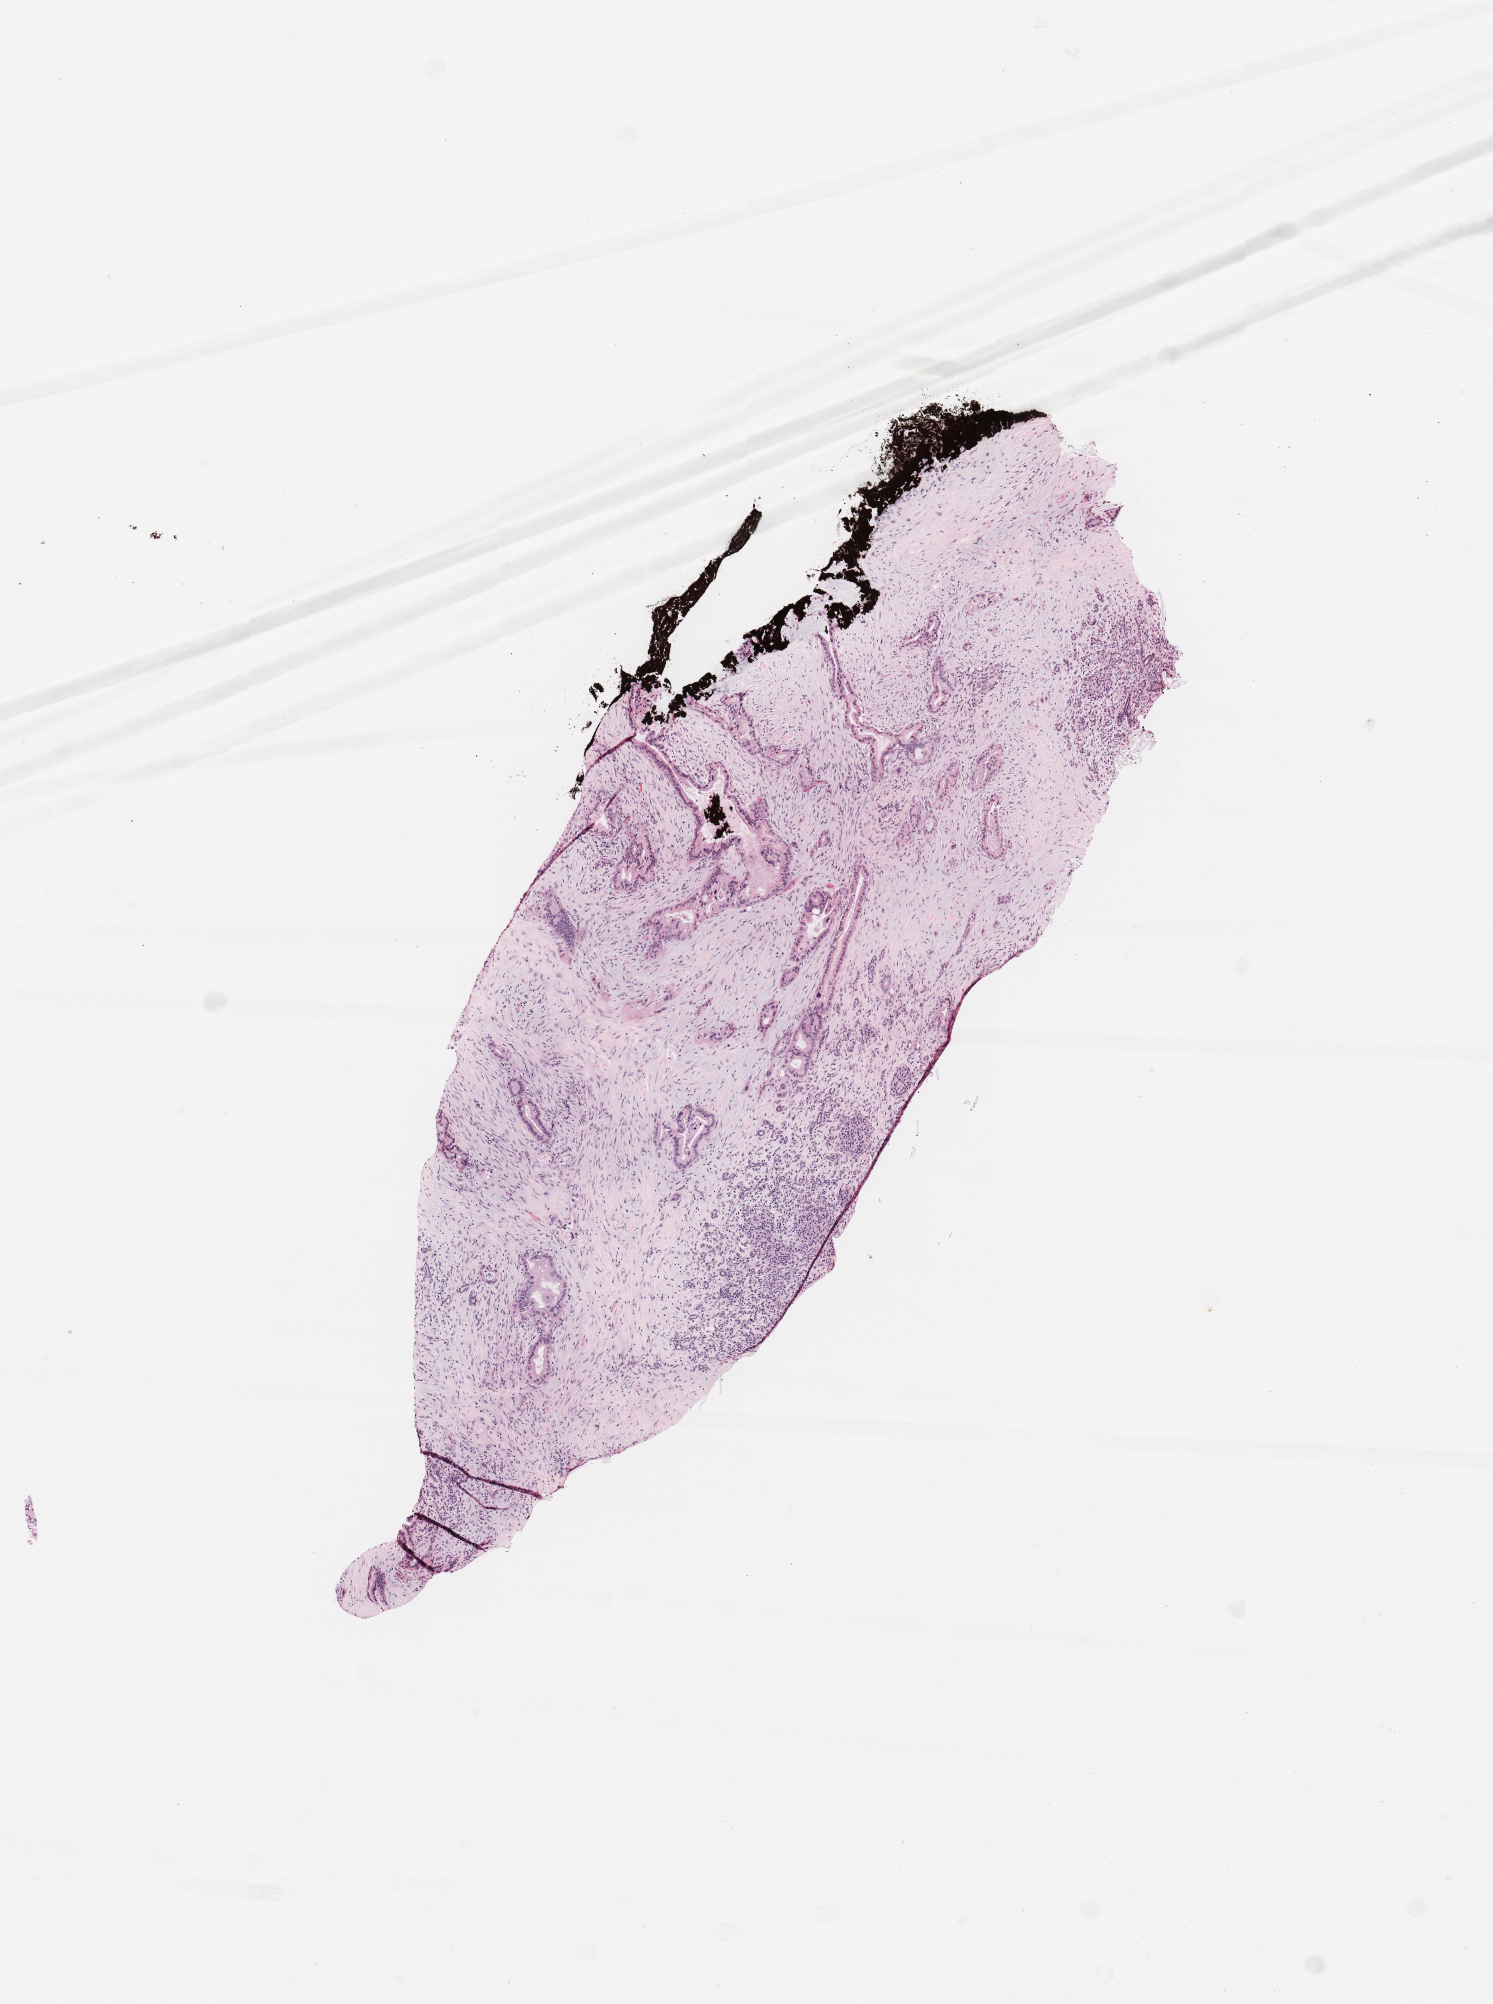
Digitized H&E tissue section (whole slide), low-resolution overview of the scanned area, about 5.9 x 7.9 mm (acquisition: 20x scan), tumour tissue sample, sampled site: pancreas. Patient: female, age 36 years. Histologic grade: G2 (moderately differentiated). Composition of this section per pathologist review: tumour nuclei 40%, necrosis 0%.
* AJCC pathologic stage: III
* diagnosis: Infiltrating duct carcinoma, NOS